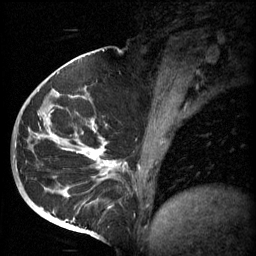
Breast MRI (dynamic contrast-enhanced), one sagittal slice; position 30 of 60 along the scan axis; 3 images stored at this slice position (order not interpretable as contrast timing); 1.5 T; TE 4.2 ms, TR 11 ms; 2 mm slice thickness; 256 × 256 image matrix. Female patient, age 51 years.
Annotated regions visible in this slice (semi-automatically segmented with operator editing):
- analysis volume of interest (the breast-tissue region the enhancement analysis was run in; not a lesion): box from (x=48, y=82) to (x=161, y=197) px
- tumour enhancement mask (voxels above the 70 % enhancement threshold inside the analysis volume of interest): (x=59, y=96)–(x=142, y=197)